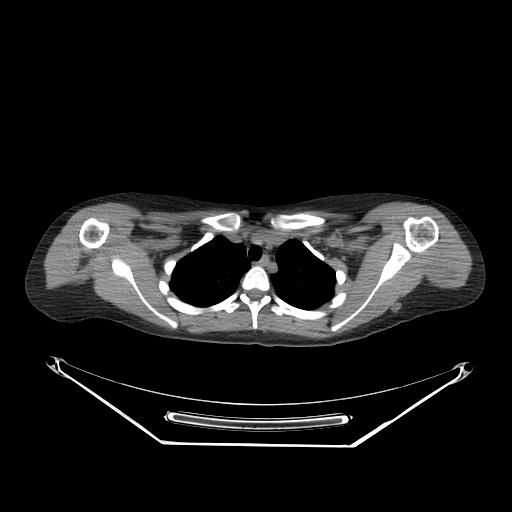
CT of an extremity soft-tissue mass (from a PET/CT study), one axial slice. Position 210 of 267 along the scan axis. Reconstruction kernel SOFT. 140 kVp. Soft-tissue window (W 400 / L 40 HU). 512 × 512 image matrix, field of view 500 × 500 mm. Female patient. Case-level facts recorded for this patient, not image findings: histological type: malignant fibrous histiocytoma; grade: low; site of the primary tumour: left arm.
Structures marked on this image (expert contour drawn on MRI and transferred to this co-registered scan by the dataset authors):
- gross tumour volume (mass): bounding box <427,254,455,282> (left, top, right, bottom; pixels)